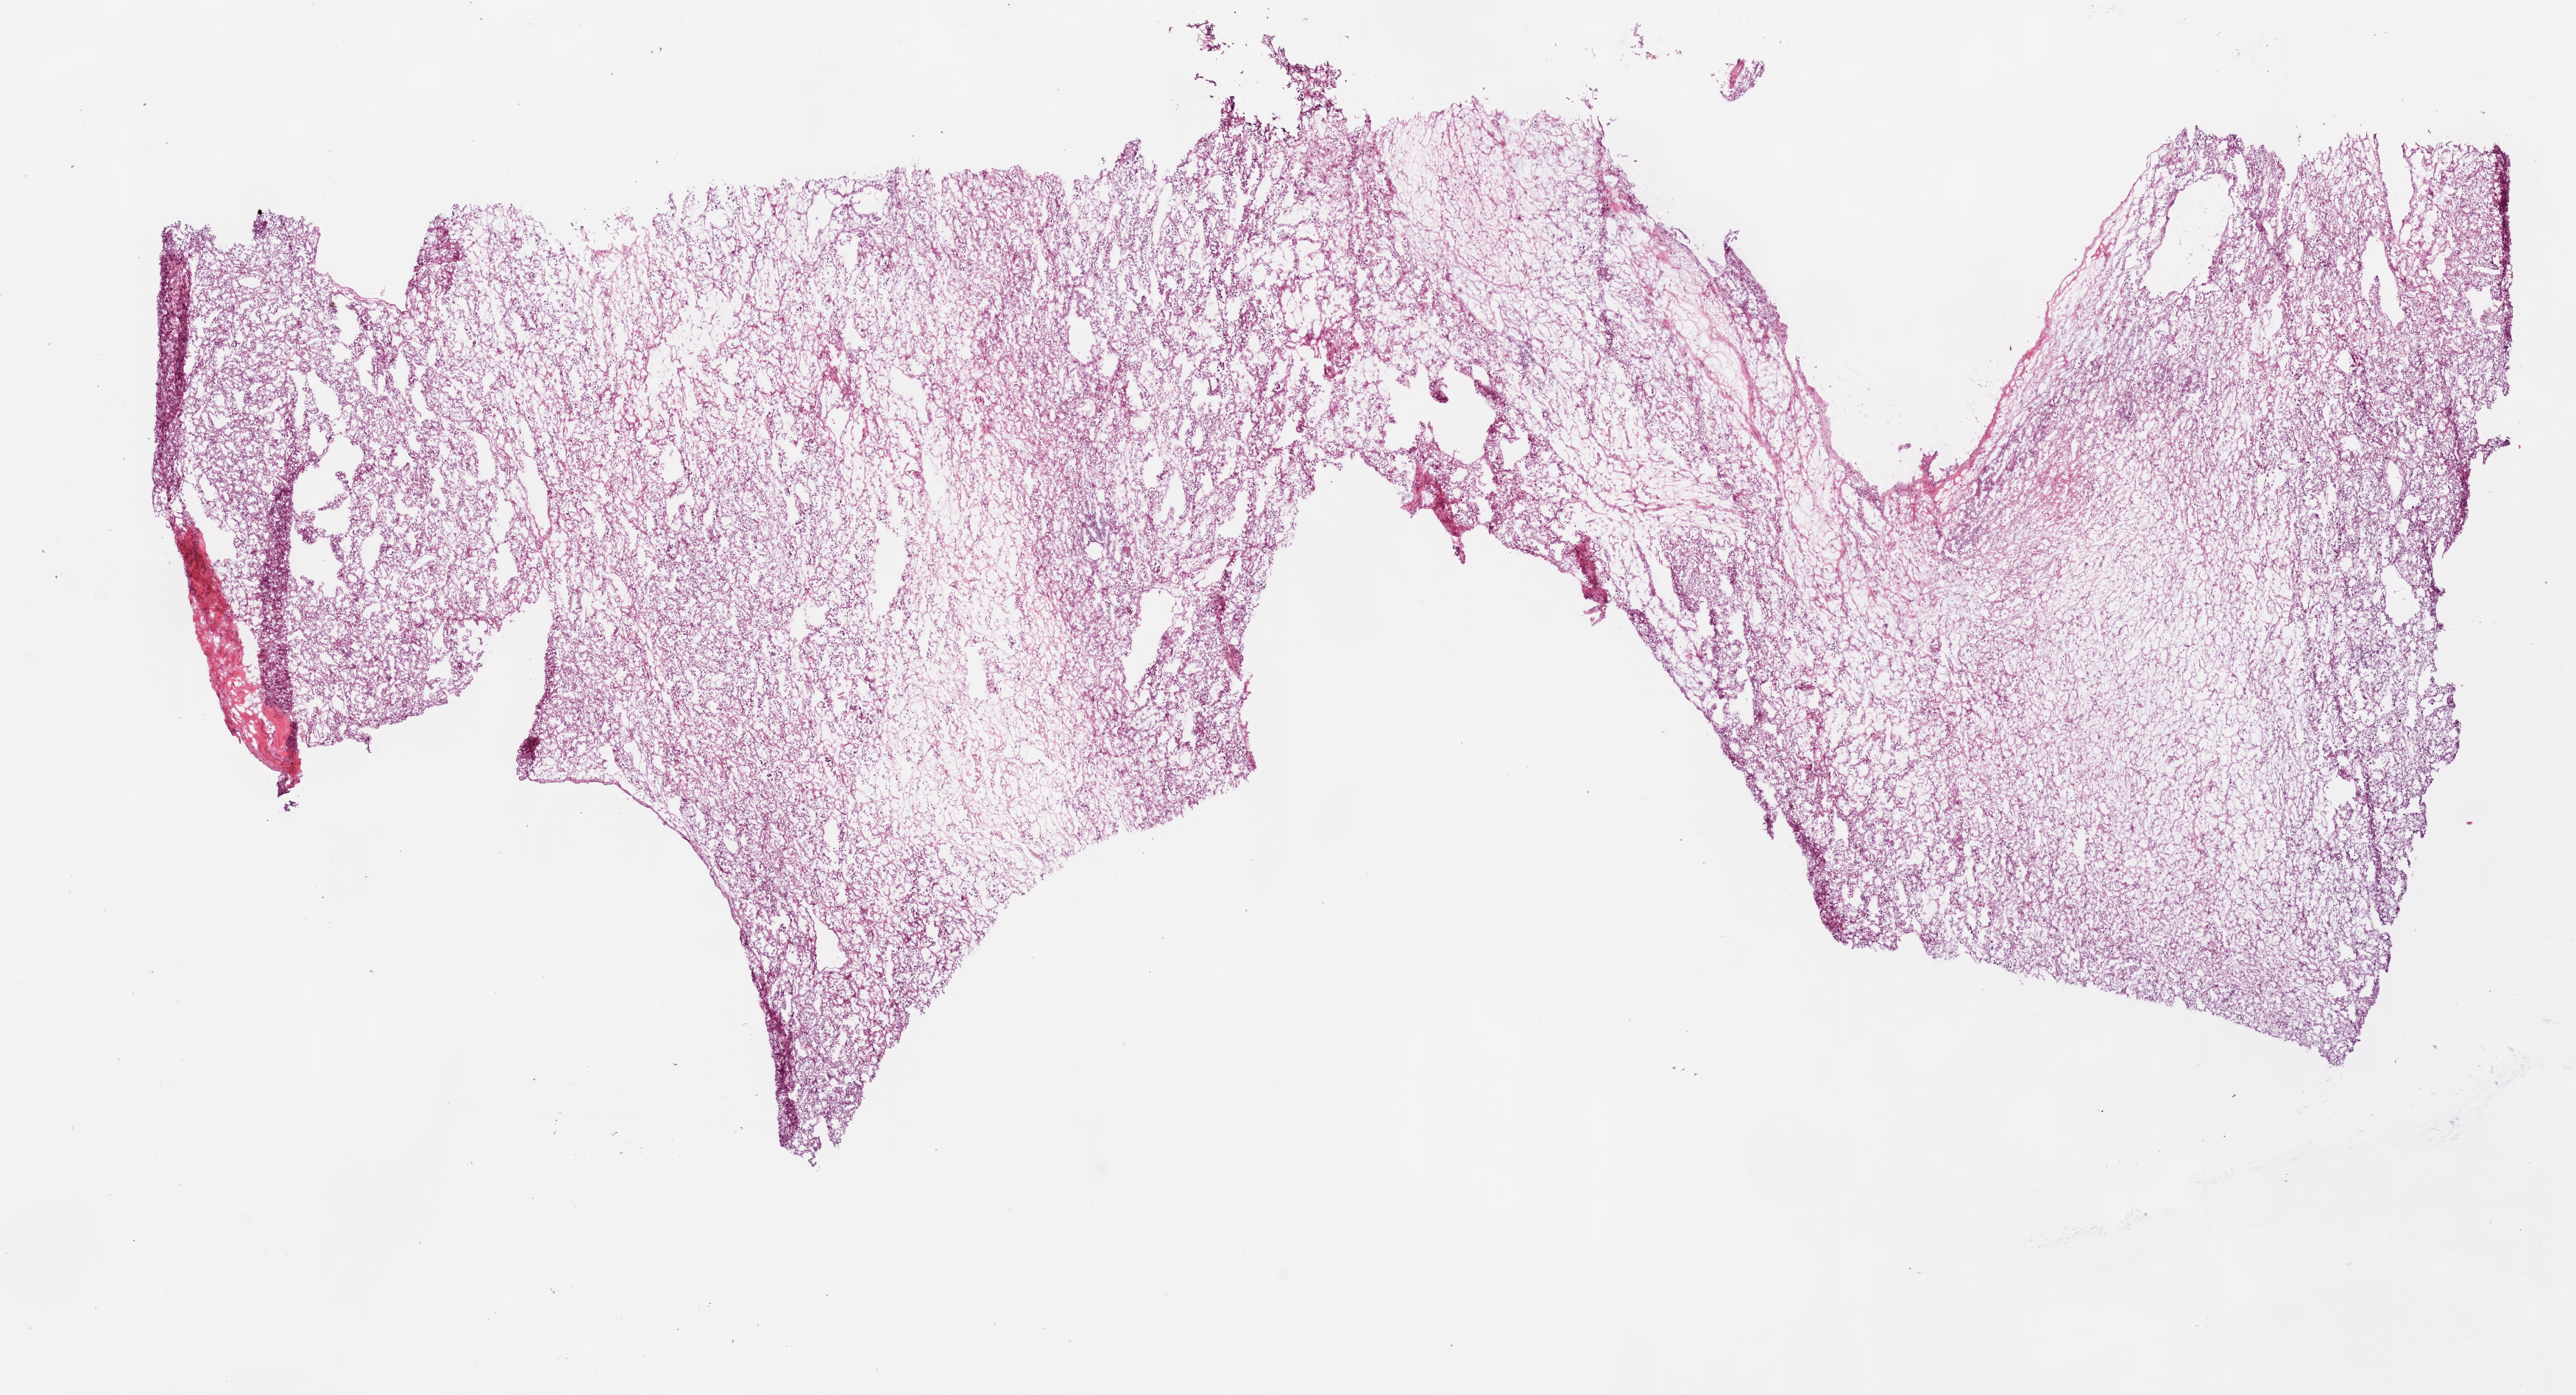
Whole-slide histology image, H&E-stained — low-resolution overview of the scanned area, about 14.0 x 7.6 mm (slide scanned at 20x); frozen section from the bottom of the tissue portion; sample: primary tumour, kidney. Patient: male, age at initial diagnosis 54 years. Histologic grade: G2 (moderately differentiated). Slide review estimates, as recorded: tumour cells 70%, tumour nuclei 80%, normal cells 0%, stromal cells 30%, necrosis 0%.
Diagnosis: Clear cell adenocarcinoma, NOS. AJCC pathologic stage: III.